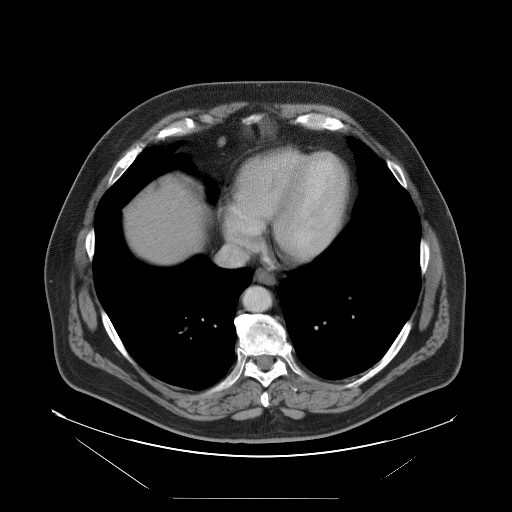
Contrast-enhanced abdominal CT, one axial slice; intravenous contrast given; soft-tissue window (W 400 / L 40 HU); 5 mm slice thickness; 512 × 512 image matrix. Male patient, age 61 years. Case-level facts recorded for this patient, not image findings: diagnosis: colorectal cancer liver metastases, imaged before liver resection; multiple liver metastases: no; largest metastasis: 6.5 cm.
Annotated regions visible in this slice (outlined manually by an expert reader):
- hepatic veins: bounding box [x1, y1, x2, y2] px = [220, 214, 268, 266]
- liver: [126, 181, 202, 265]
- planned liver remnant (the part of the liver to remain after resection): [165, 180, 203, 233]